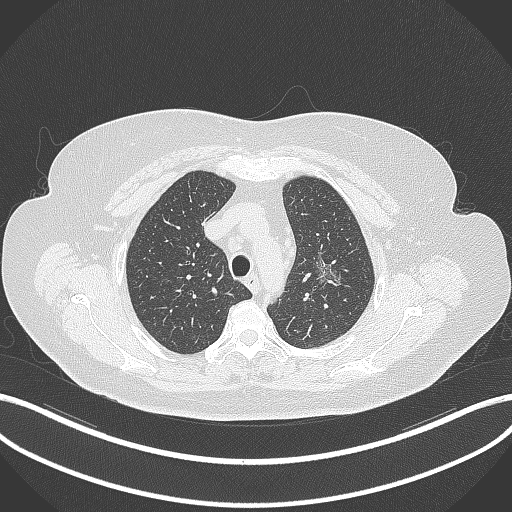
Chest CT, one axial slice; slice 262 of 309 in the series (ordered by position); reconstruction kernel B70f; lung window (W 1500 / L -600 HU); 1 mm slice thickness; 512 × 512 image matrix. Patient: female, 70 years. From the clinical record (not read from this slice): clinical TNM (as recorded): T1c N0 M0.
Annotated regions visible in this slice (bounding box drawn by a radiologist):
- lung tumour (recorded histology: adenocarcinoma): bounding box [x1, y1, x2, y2] px = [314, 253, 344, 293]